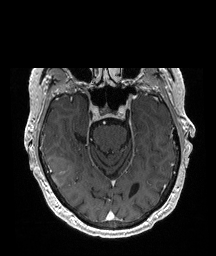
Brain MRI from a brain-tumour surgery series, one axial slice; slice 138 of 208 in the series (ordered by position); T1-weighted post-contrast; 216 × 256 image matrix, field of view 216 × 256 mm. From the clinical record (not read from this slice): histopathology: Glioblastoma; WHO grade: 4; IDH mutation: no.
Structures marked on this image (outlined manually by an expert reader):
- tumour: bounding box [x1, y1, x2, y2] px = [47, 156, 72, 187]